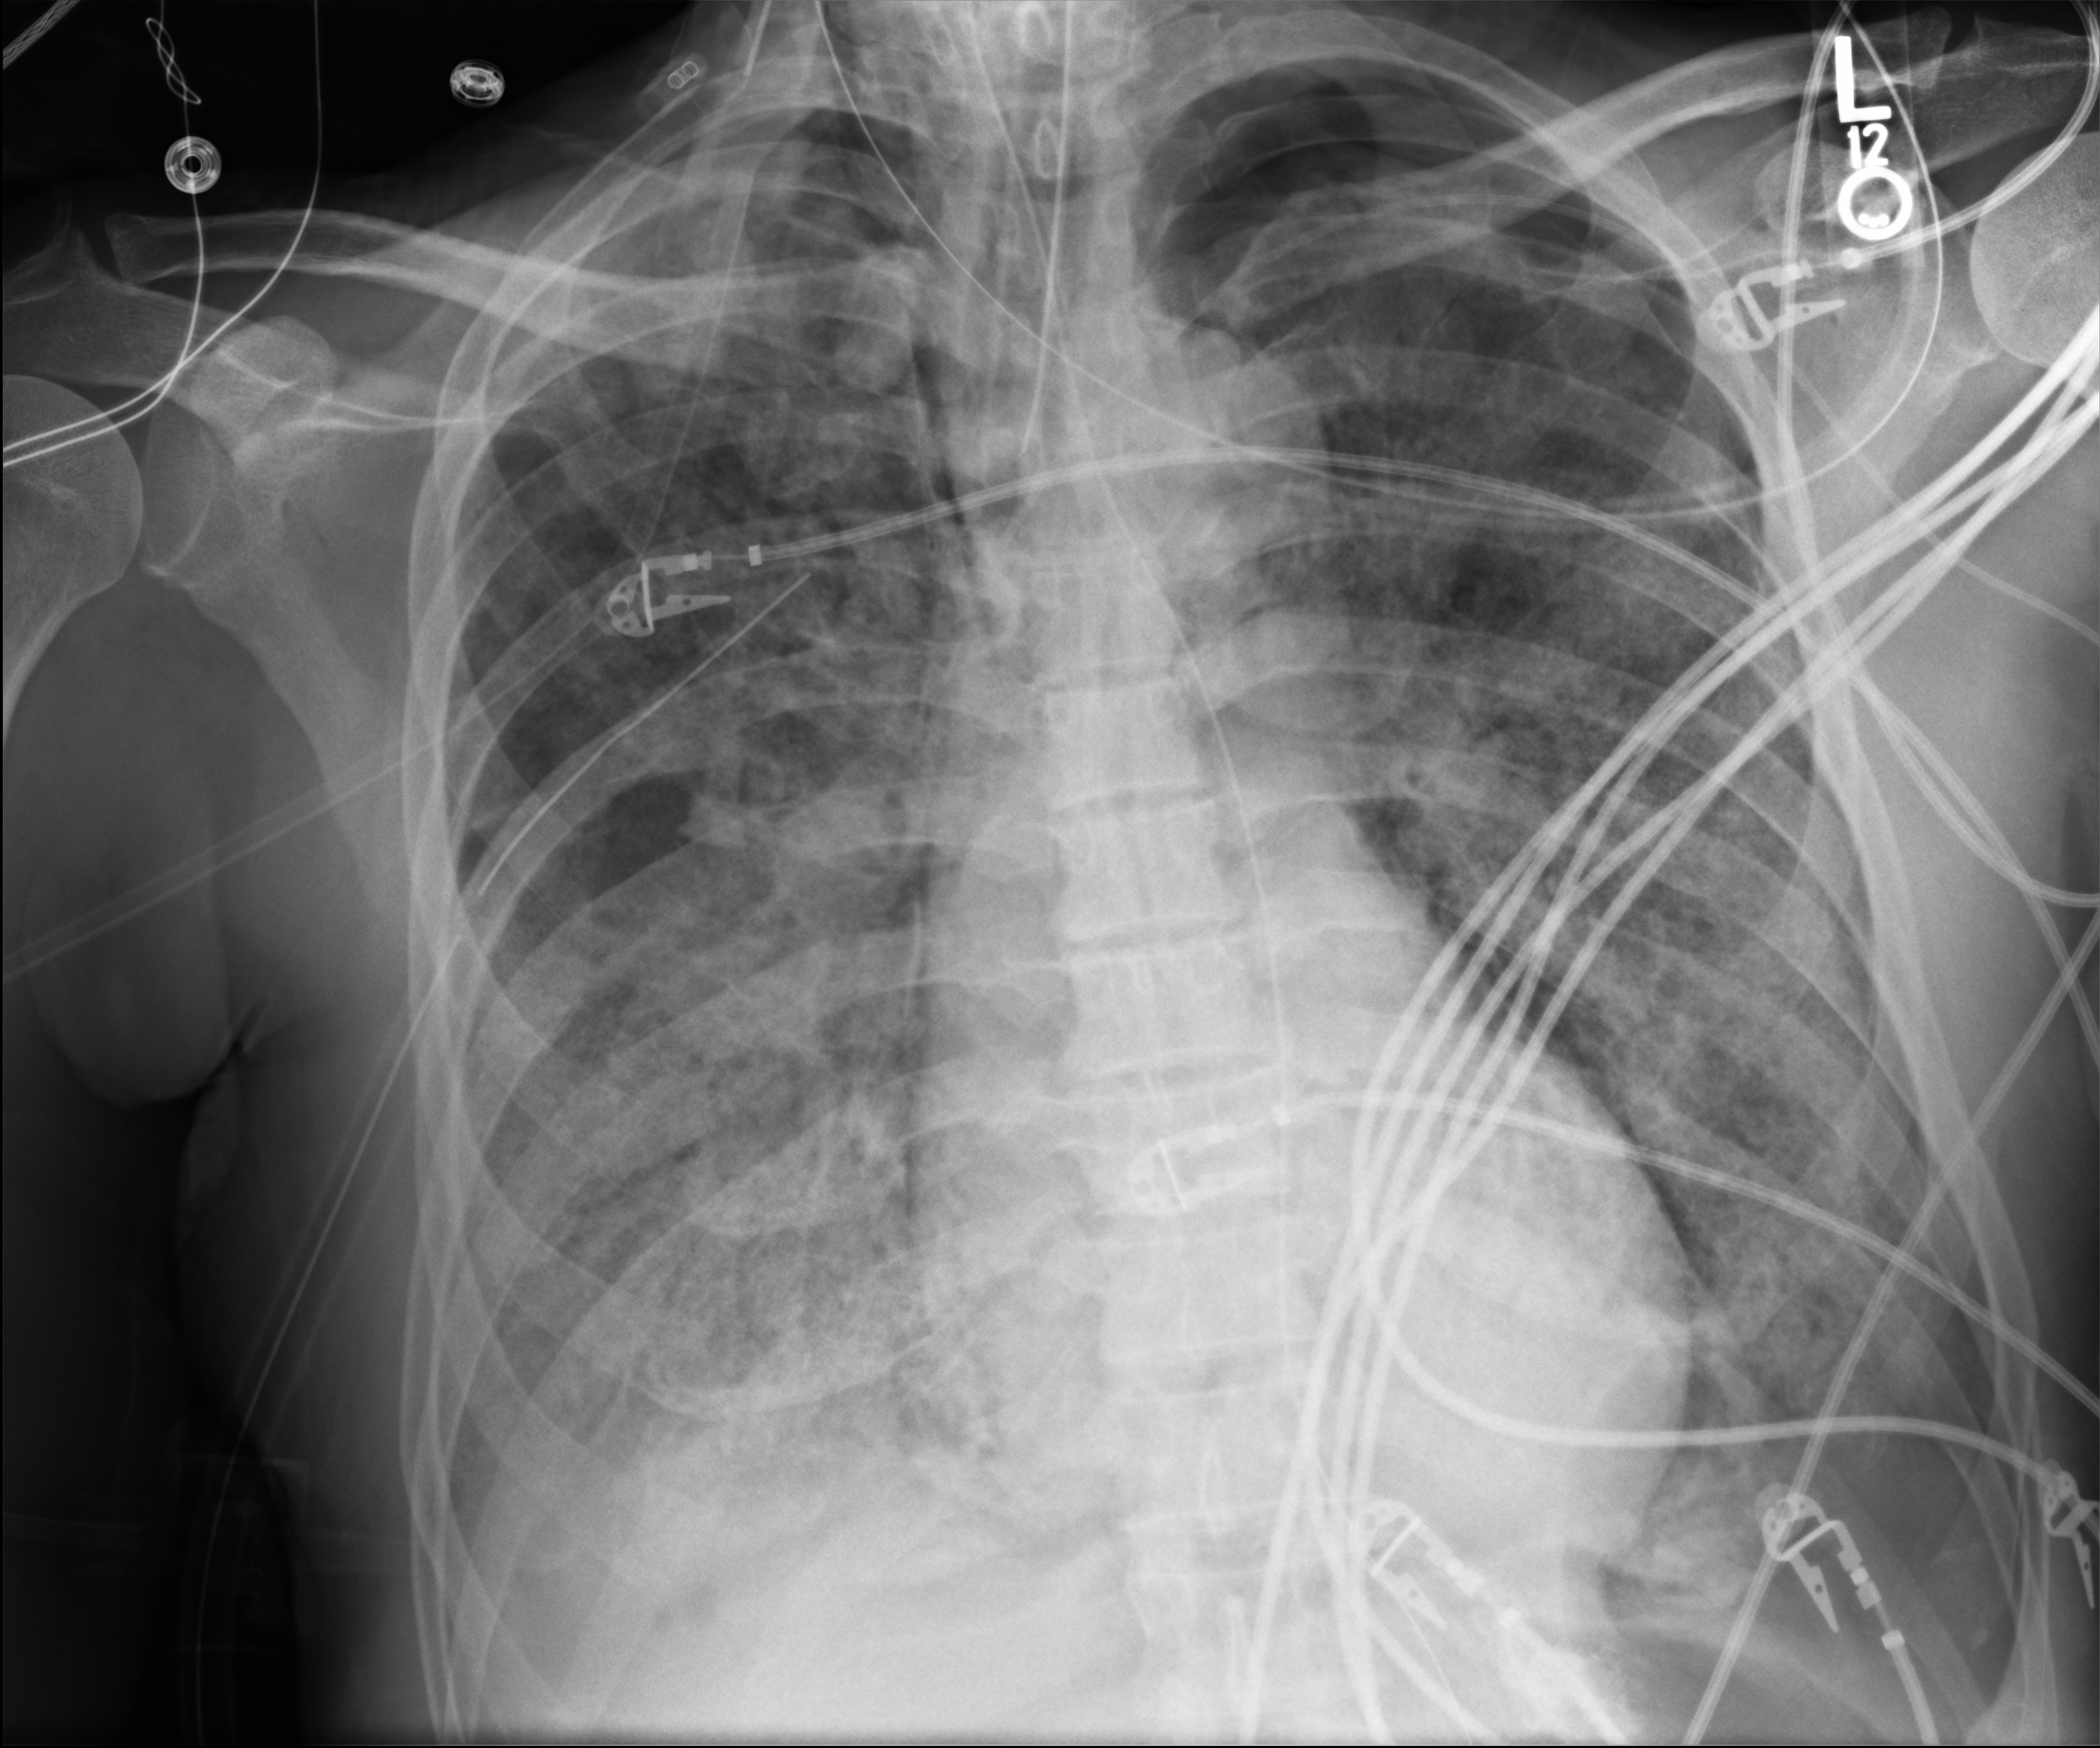
Bedside chest radiograph (computed radiography), anteroposterior (AP) projection. Male patient hospitalised with COVID-19, age 60–74 years.
Hospital-stay facts (about this admission, not read from this image; timing relative to this image not recorded):
- chronic kidney disease (admission record): no
- admitted to intensive care during this hospital stay: yes